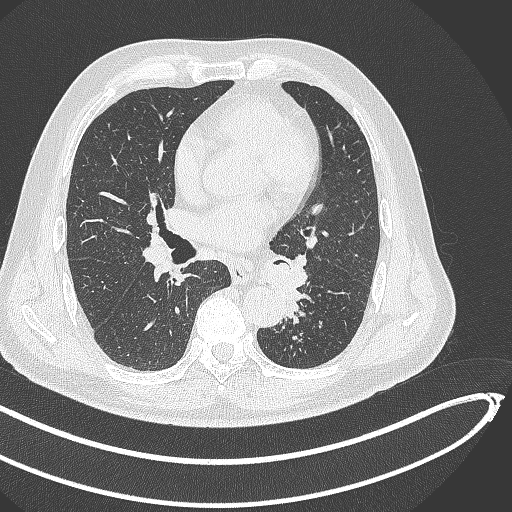
Chest CT, one axial slice. Position 243 of 468 along the scan axis. Lung window (W 1500 / L -600 HU). 1 mm slice thickness. 512 × 512 image matrix, field of view 400 × 400 mm. Male patient, age 64 years. Case-level facts recorded for this patient, not image findings: clinical TNM (as recorded): T1c N0 M0; histopathological grade: G2.
Annotated regions visible in this slice (bounding box drawn by a radiologist):
- lung tumour (recorded histology: squamous cell carcinoma): bounding box (x1, y1, x2, y2) in pixels: (260, 258, 302, 316)